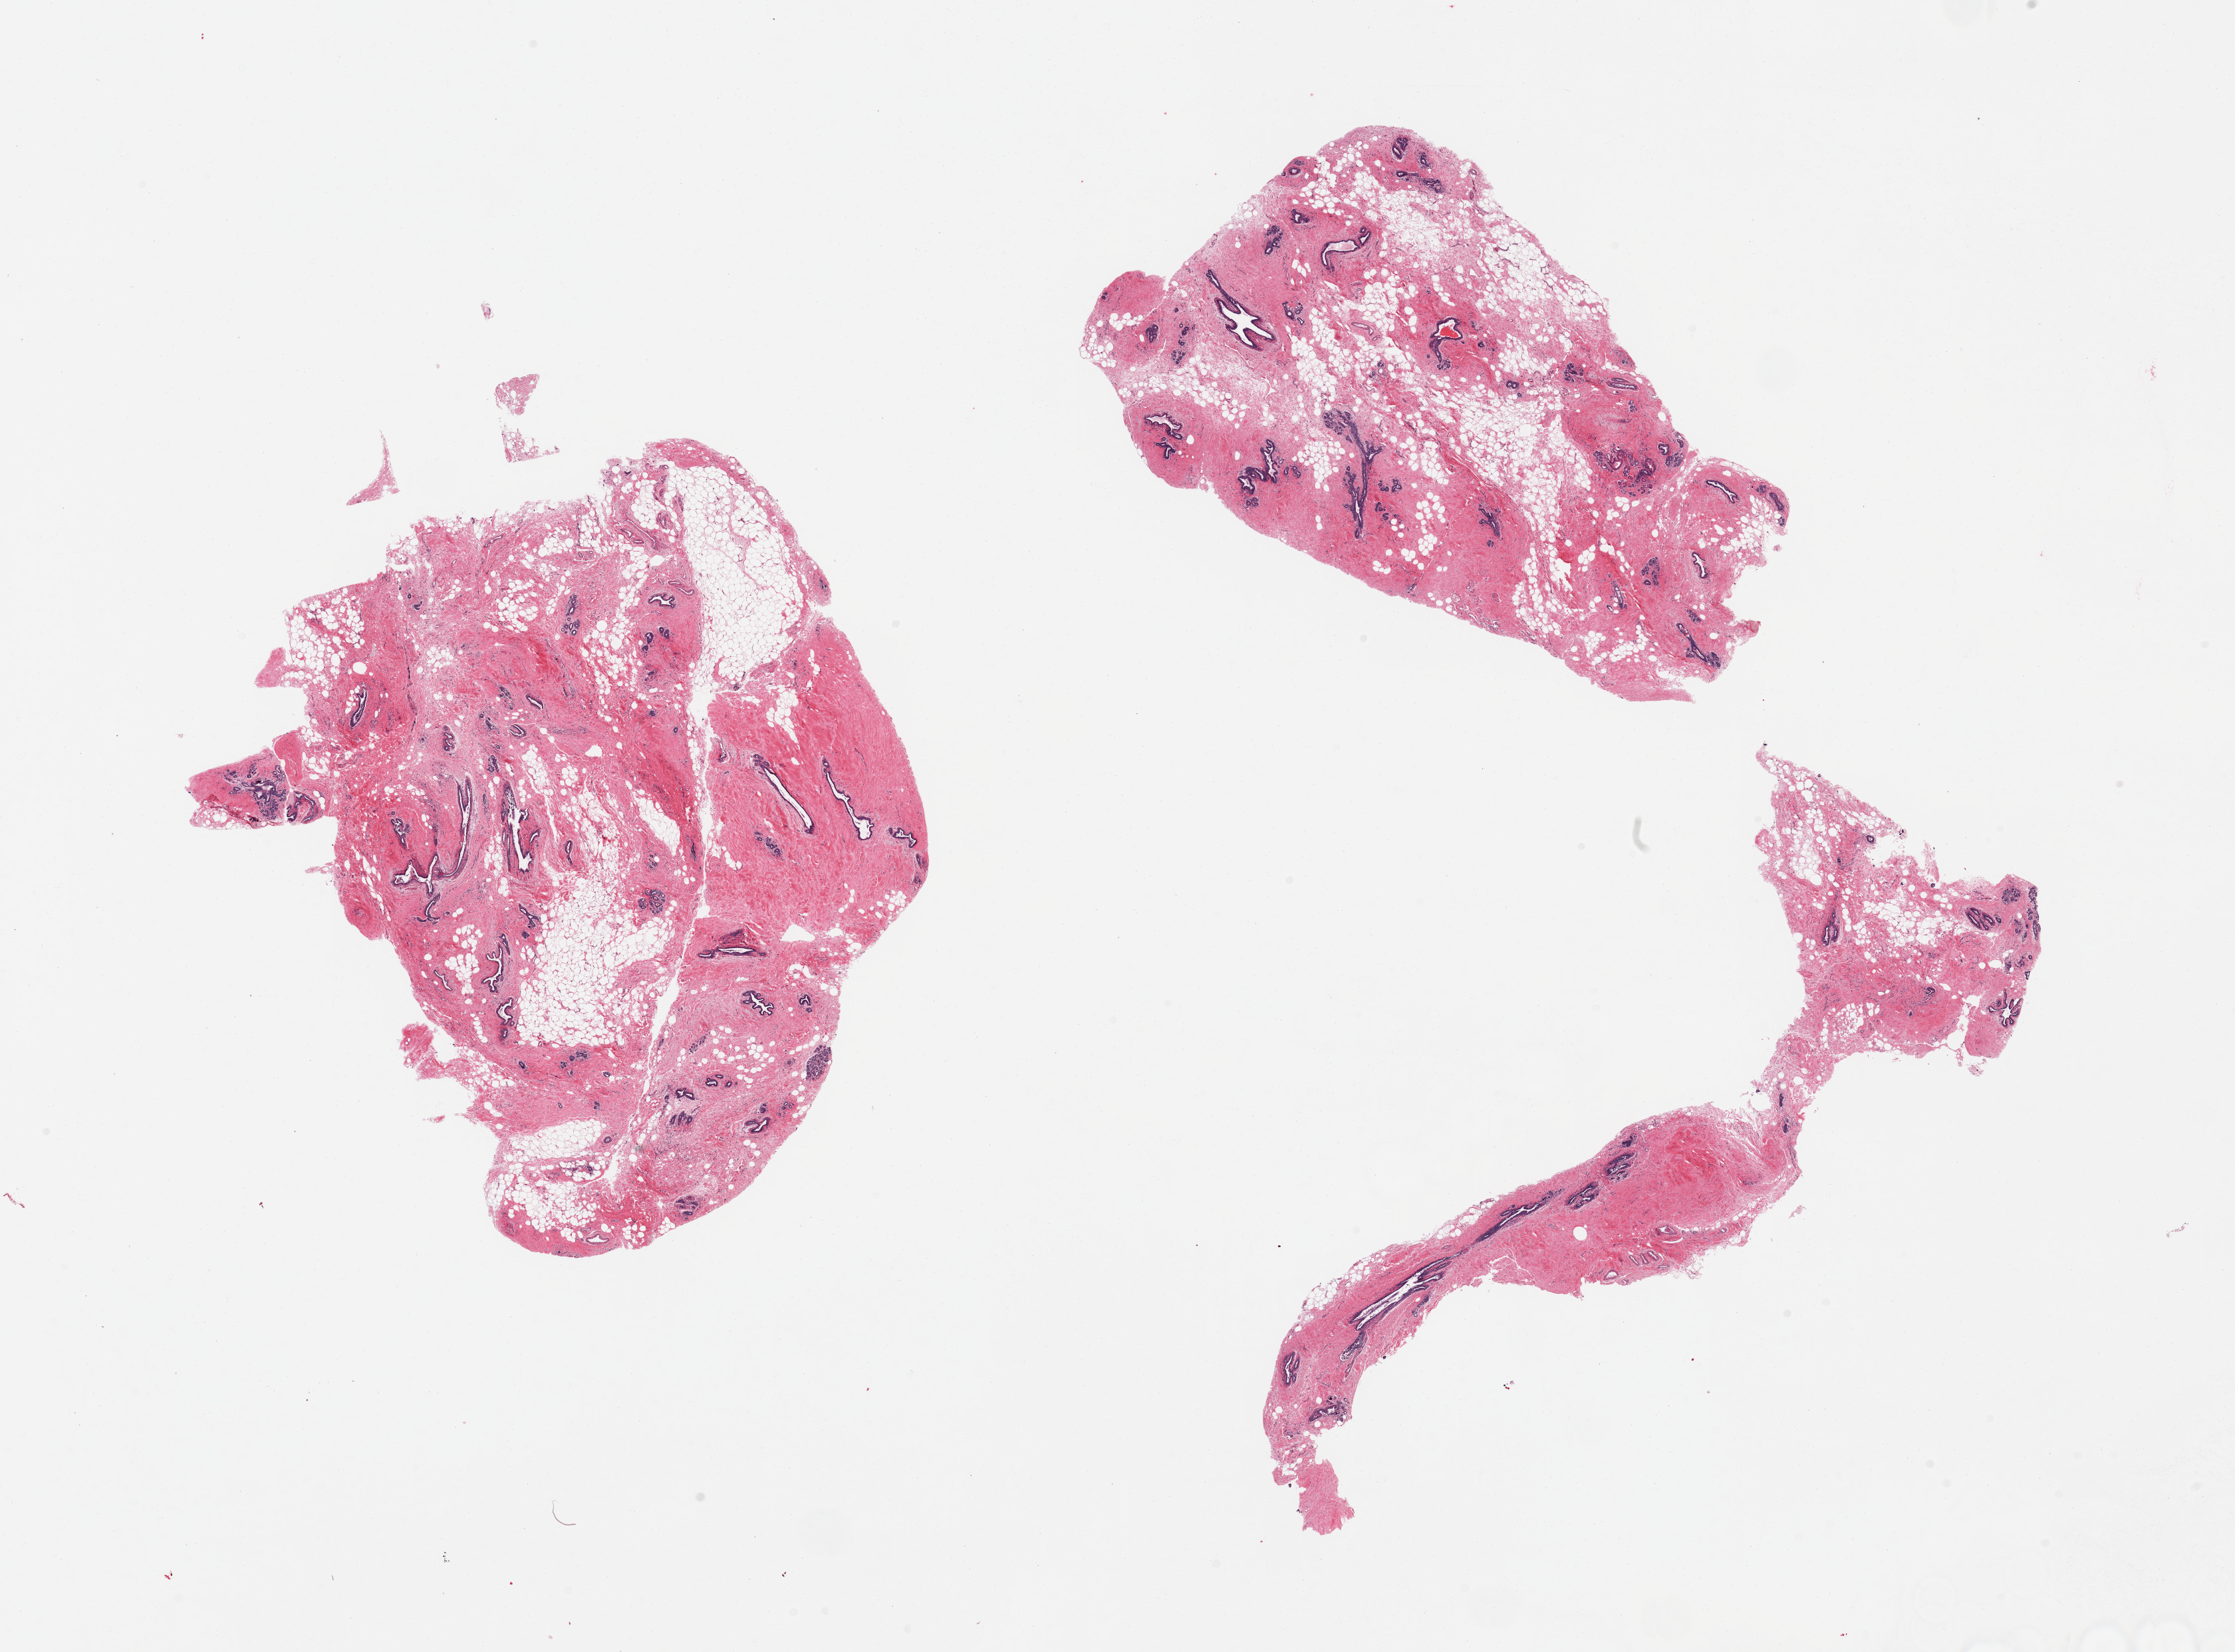
Whole-slide image, H&E stain — shown as a low-resolution overview of the whole scanned area (about 26.6 x 19.7 mm, from a 20x scan). PAXgene-fixed, paraffin-embedded tissue. Target tissue: breast. Tissue donor sample. Donor sex: female.
Reviewer comment on this tissue sample: 3 pieces; some fibrocystic change.